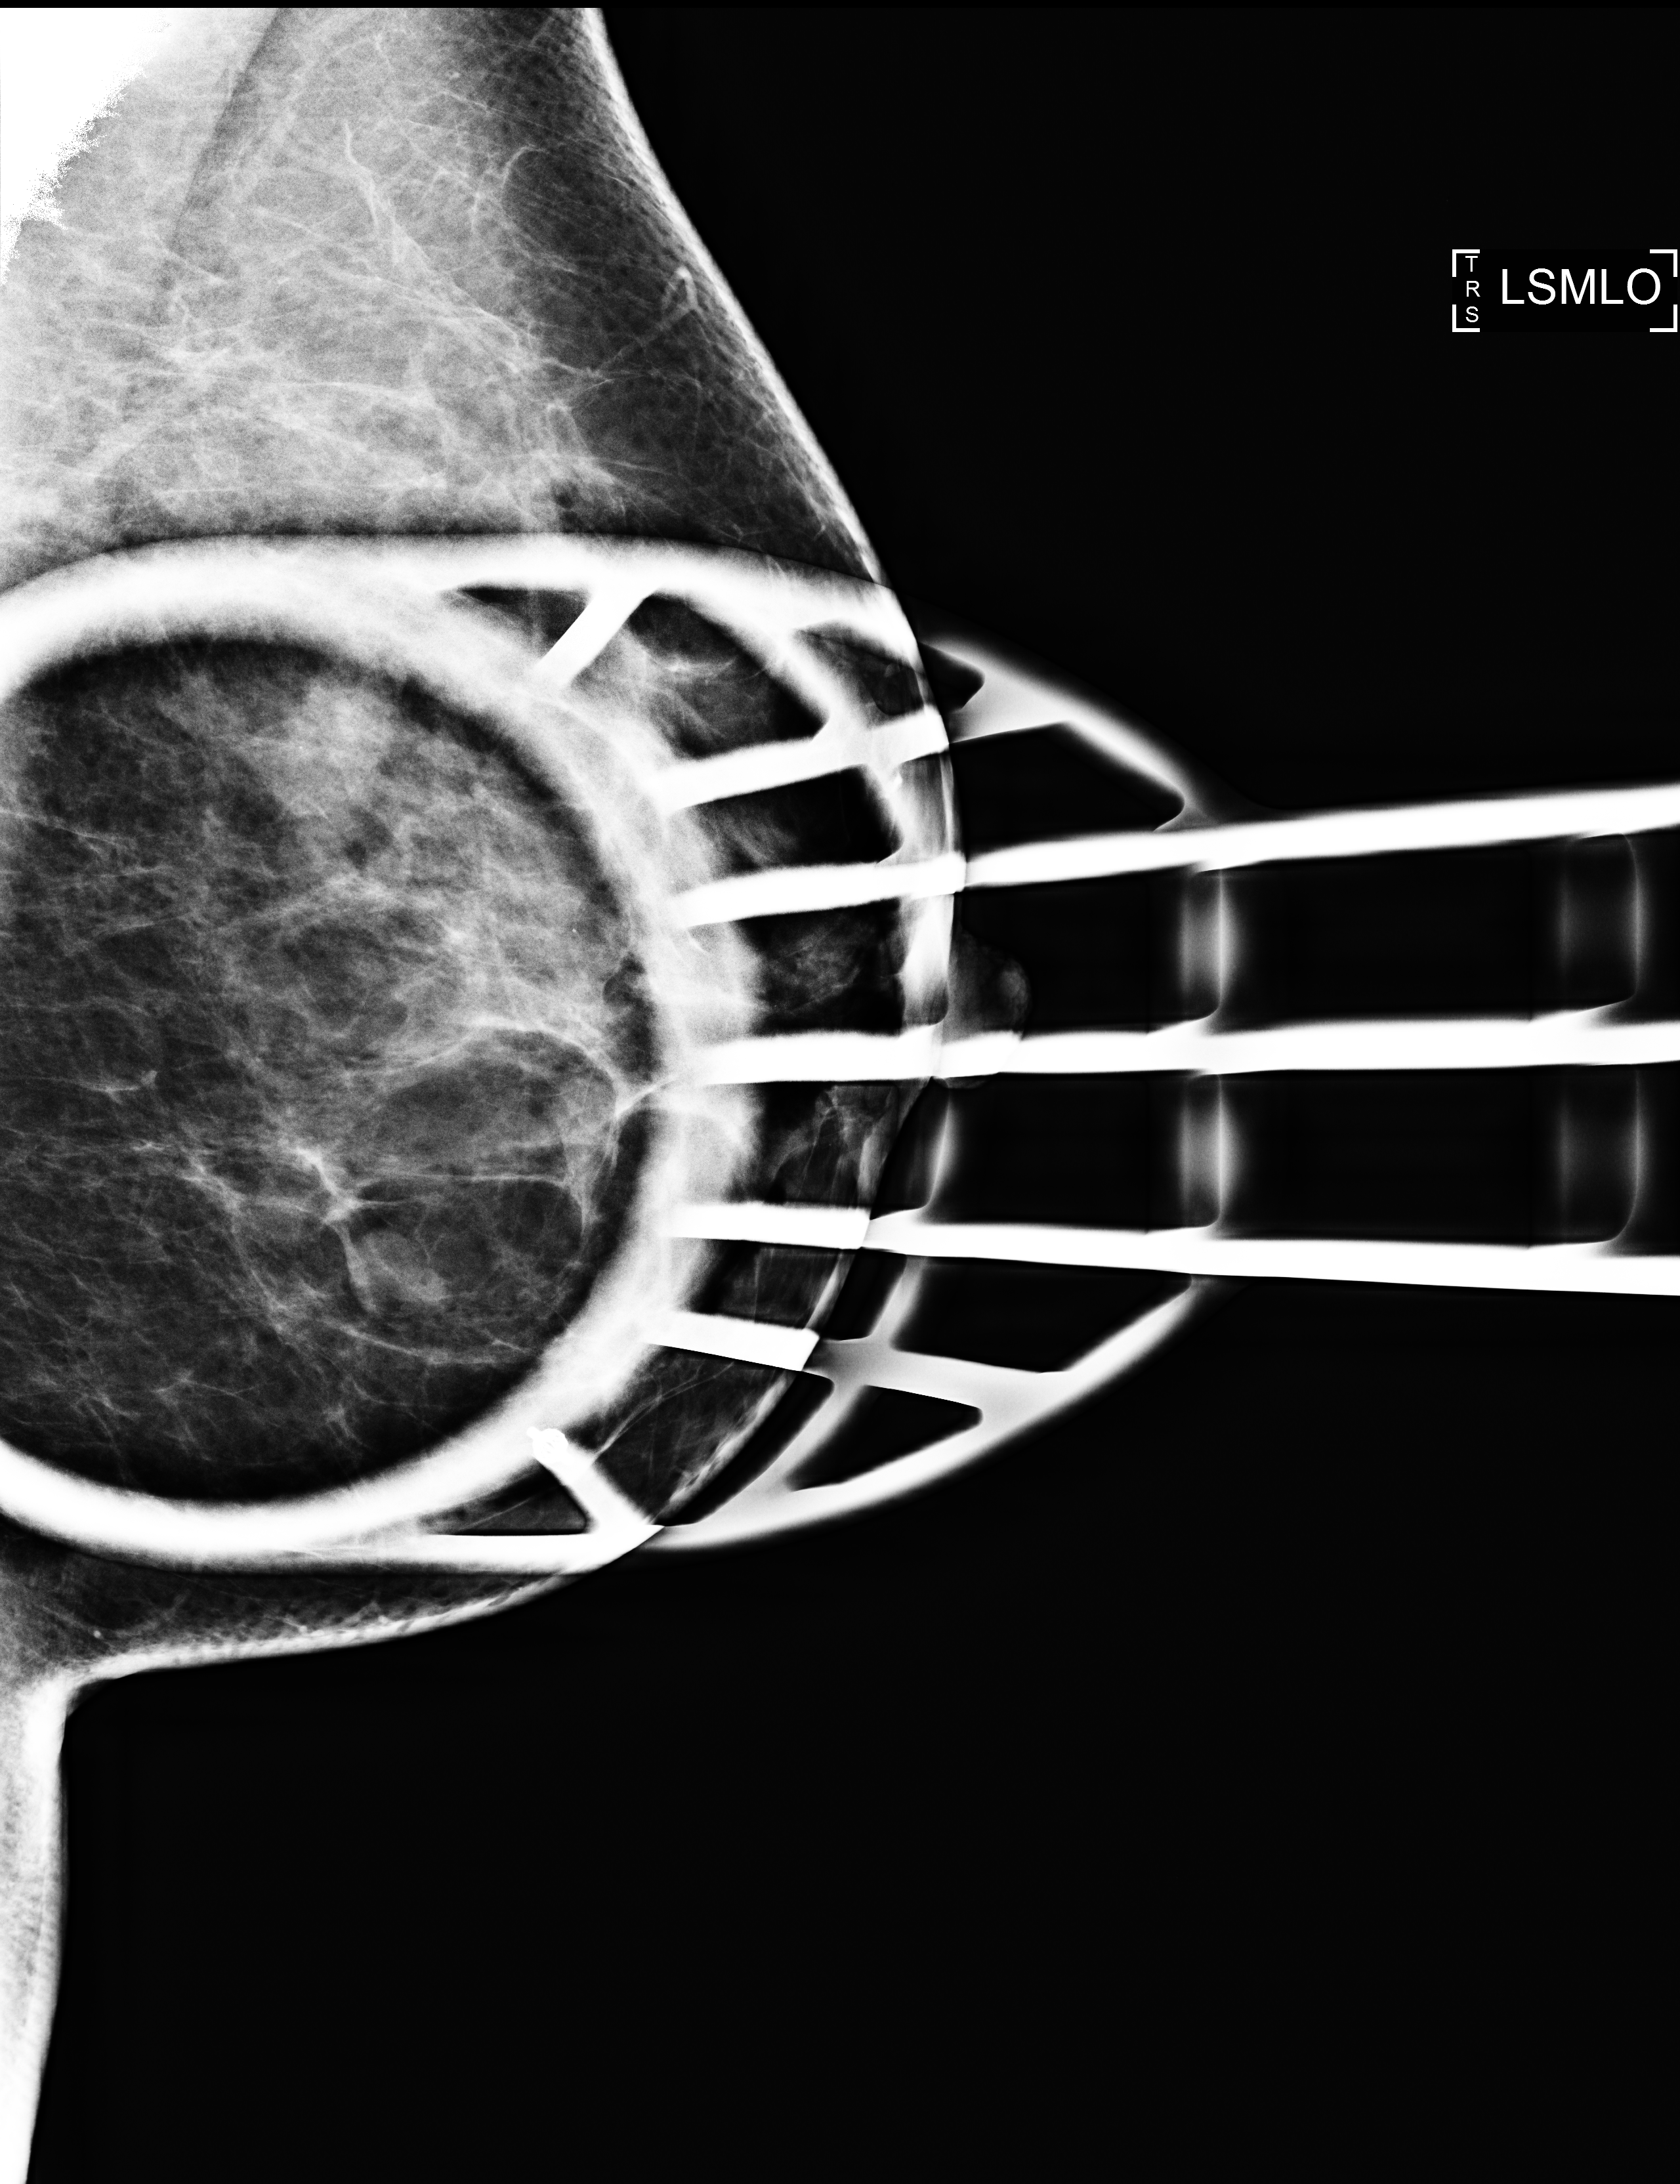
Additional work-up view. Patient aged 42 years (female).
Image type: full-field digital mammogram. Breast: left. Projection: MLO view, spot compression.